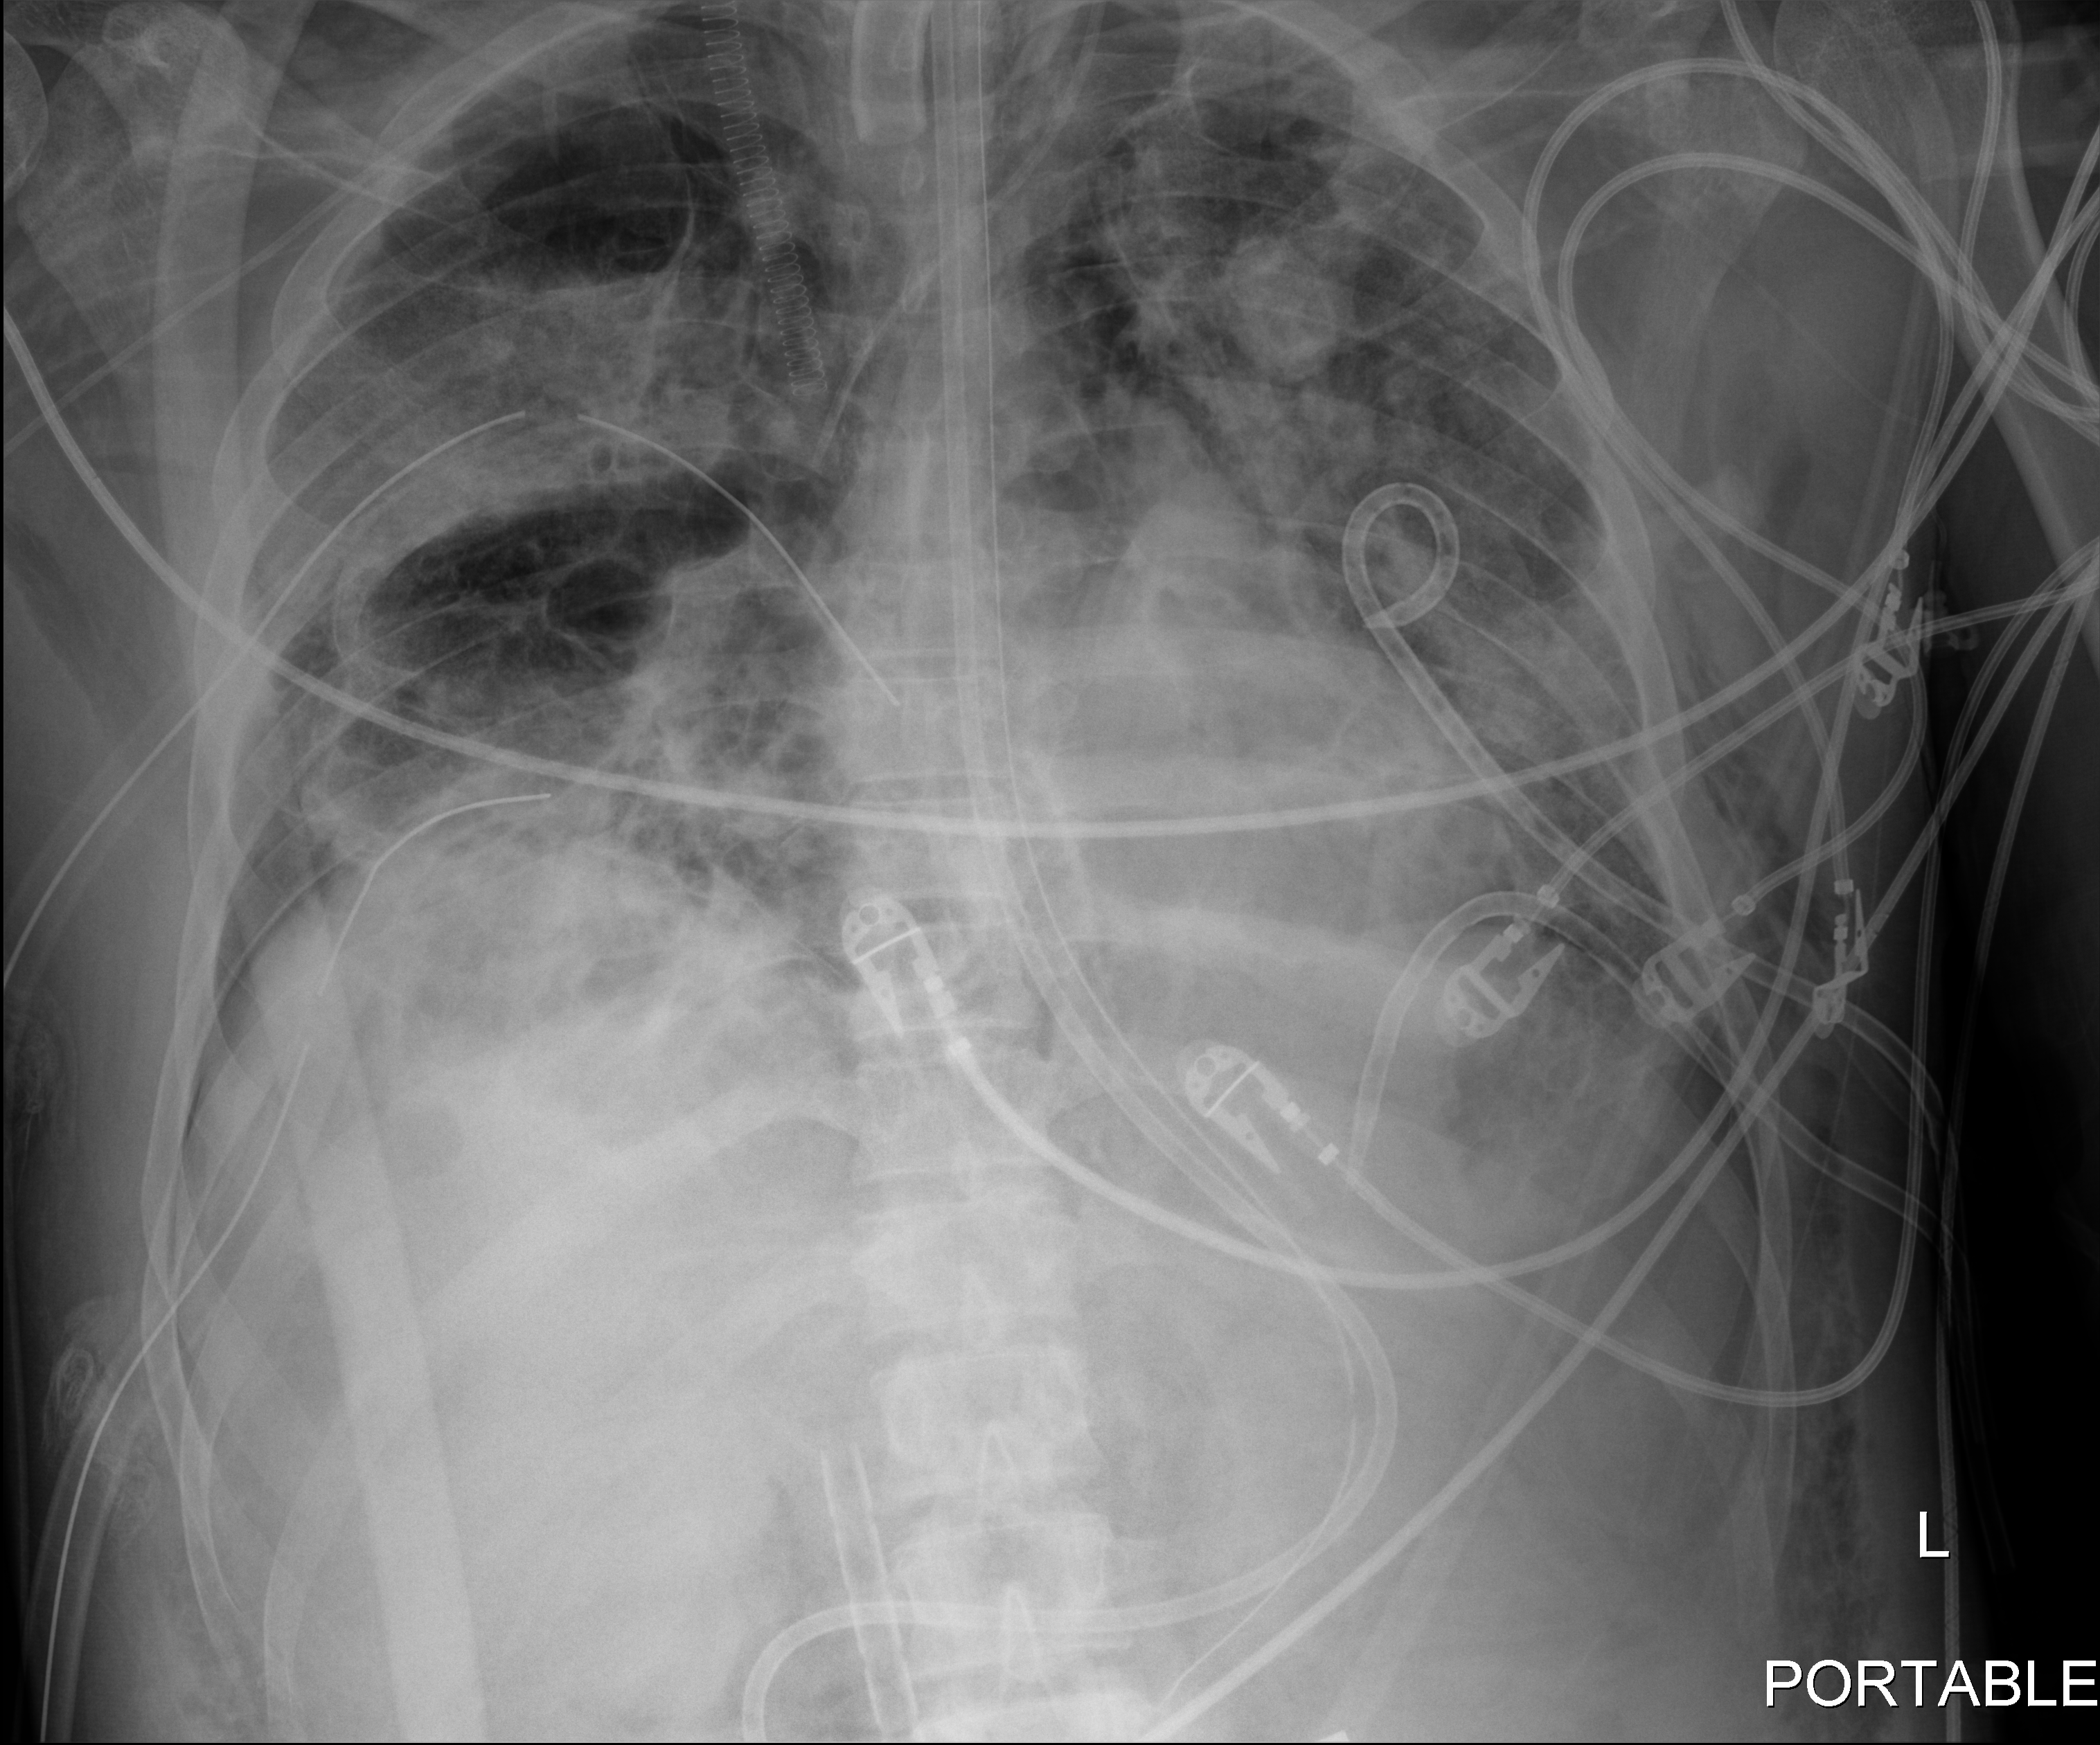
Chest X-ray; anteroposterior (AP) projection. Patient hospitalised with COVID-19, aged 18–59 years.
Hospital-stay facts (about this admission, not read from this image; timing relative to this image not recorded): mechanically ventilated during this hospital stay: yes.